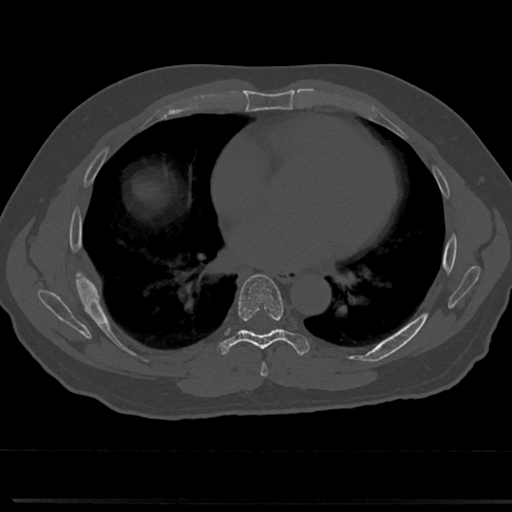
CT including the spine, one axial slice; slice 407 of 817 in the series (ordered by position); bone window (W 1800 / L 400 HU); 0.5 mm slice thickness; 512 × 512 image matrix. Patient: male, 61 years. Case-level facts recorded for this patient, not image findings: primary cancer: prostate.
Annotated regions visible in this slice (semi-automatic segmentation, software-assisted and operator-edited):
- T6 vertebra: bounding box <256,340,319,370> (left, top, right, bottom; pixels)
- T7 vertebra: <216,275,307,358>